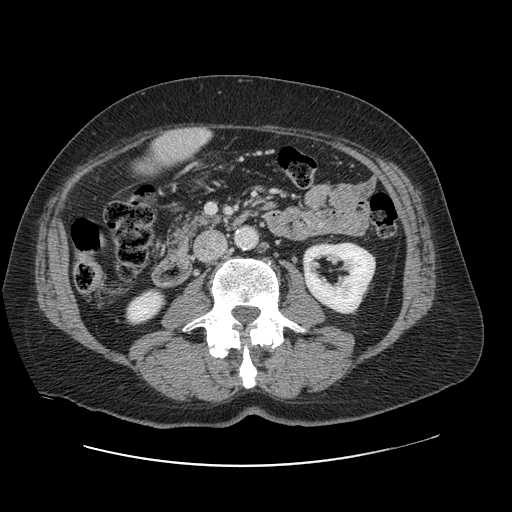
Contrast-enhanced abdominal CT, one axial slice; intravenous contrast given; soft-tissue window (W 400 / L 40 HU); 2.5 mm slice thickness; 512 × 512 image matrix, field of view 402 × 402 mm. Male patient, age 71 years. From the clinical record (not read from this slice): diagnosis: colorectal cancer liver metastases, imaged before liver resection; multiple liver metastases: no; largest metastasis: 3.3 cm; disease in both lobes: no.
Annotated regions visible in this slice (outlined manually by an expert reader):
- liver: bounding box [x1, y1, x2, y2] px = [151, 129, 210, 168]
- planned liver remnant (the part of the liver to remain after resection): [152, 144, 167, 167]